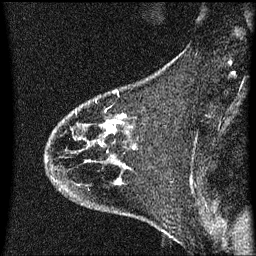
Breast MRI (dynamic contrast-enhanced), one sagittal slice. Slice 19 of 60 in the series (ordered by position). Dynamic contrast-enhanced series, image 2 of 3 at this slice position (ordered by acquisition). 1.5 T. TE 4.2 ms, TR 8.4 ms. 256 × 256 image matrix, field of view 200 × 200 mm. Female patient, age 35 years. Case-level facts recorded for this patient, not image findings: setting: breast cancer imaged before/during neoadjuvant chemotherapy; receptor status: HER2-positive.
Outlined on this slice (semi-automatic segmentation, software-assisted and operator-edited):
- analysis volume of interest (the breast-tissue region the enhancement analysis was run in; not a lesion): bounding box <45,68,174,173> (left, top, right, bottom; pixels)
- tumour enhancement mask (voxels above the 70 % enhancement threshold inside the analysis volume of interest): <110,116,125,125>